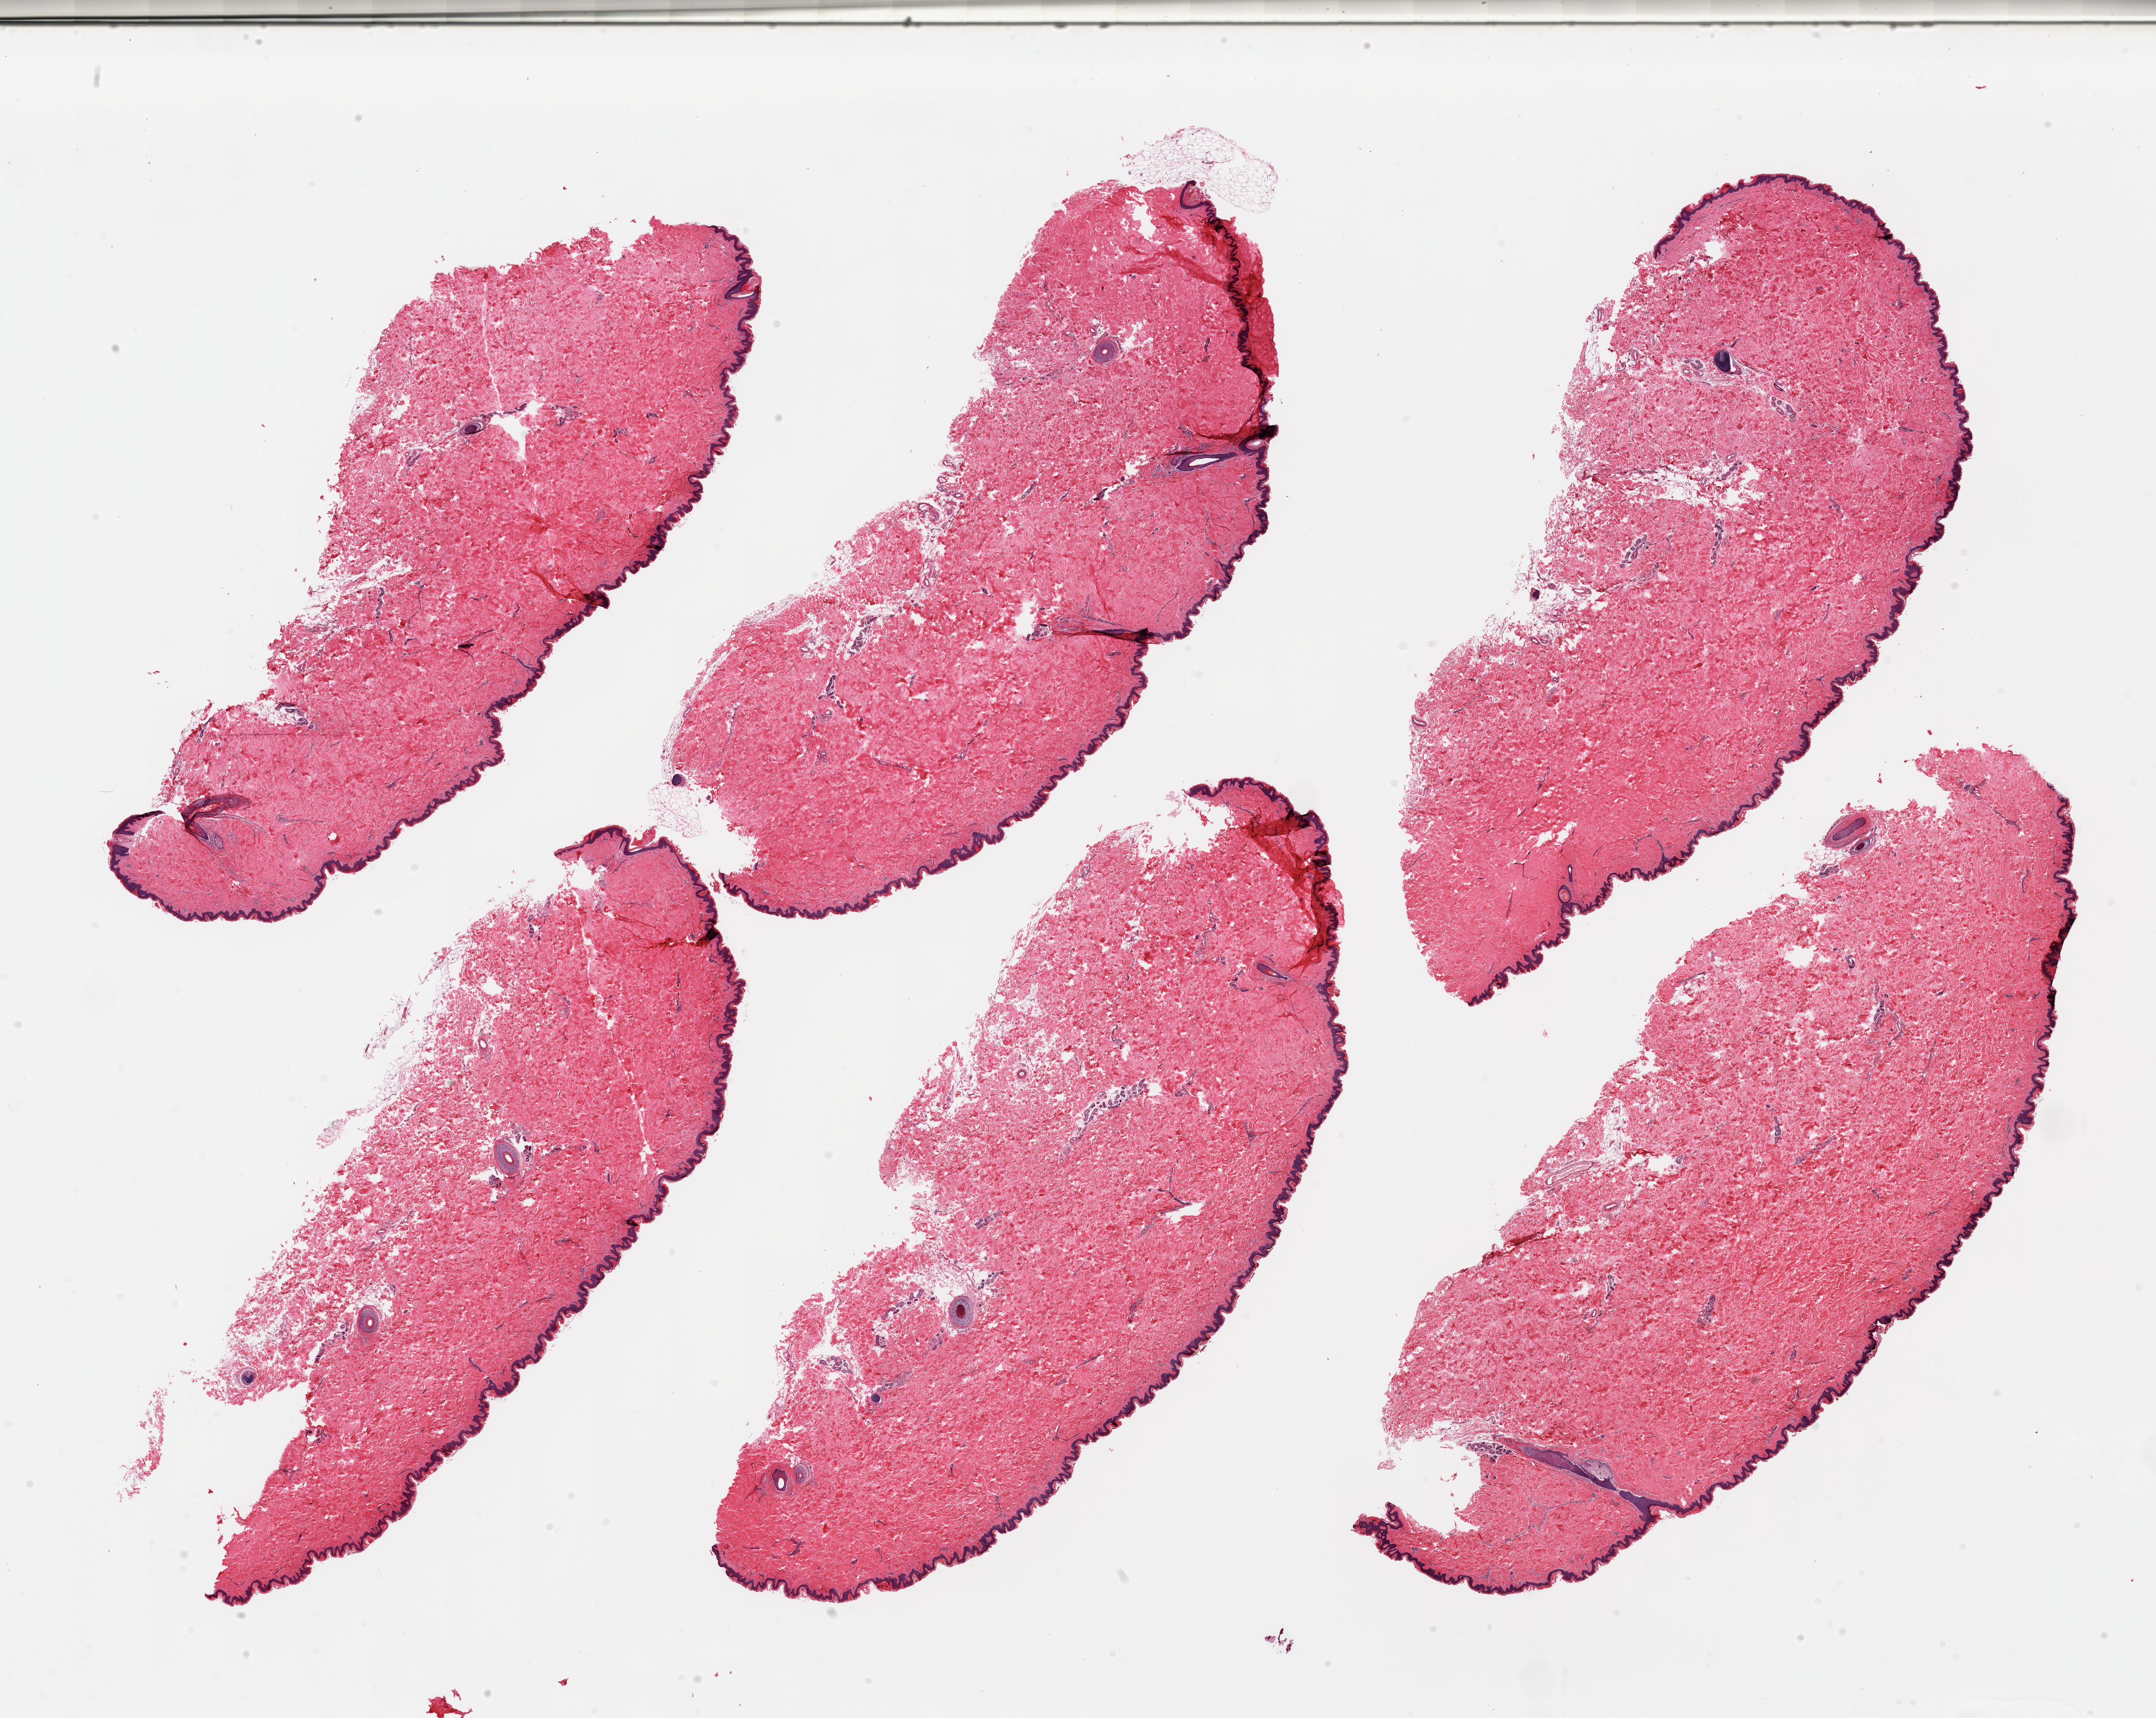
Haematoxylin and eosin whole-slide image, brightfield, shown as a low-resolution overview of the whole scanned area (about 28.5 x 22.8 mm). PAXgene-fixed, paraffin-embedded tissue. Target tissue: skin of suprapubic region. Donor tissue sample. Female donor.
- review note (as recorded): 6 pieces only trace dermal fat; squamous epithelium is ~70 microns